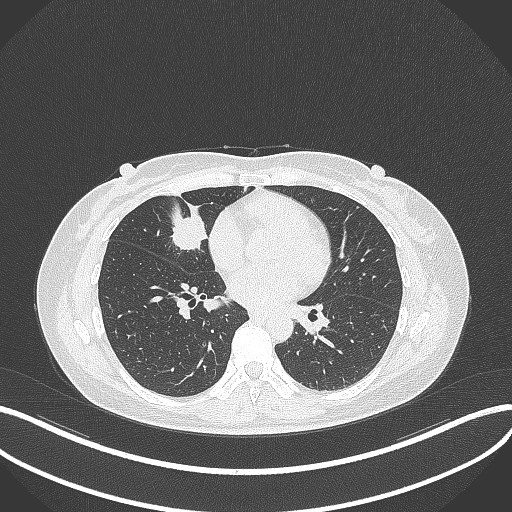
Chest CT, one axial slice; slice 131 of 284 in the series (ordered by position); reconstruction kernel B70f; 120 kVp; lung window (W 1500 / L -600 HU); 1 mm slice thickness; 512 × 512 image matrix. Female patient, age 43 years. From the clinical record (not read from this slice): clinical TNM (as recorded): T1c N3 M1; histopathological grade: G1.
Annotated regions visible in this slice (bounding box drawn by a radiologist):
- lung tumour (recorded histology: adenocarcinoma): bounding box <169,202,210,253> (left, top, right, bottom; pixels)